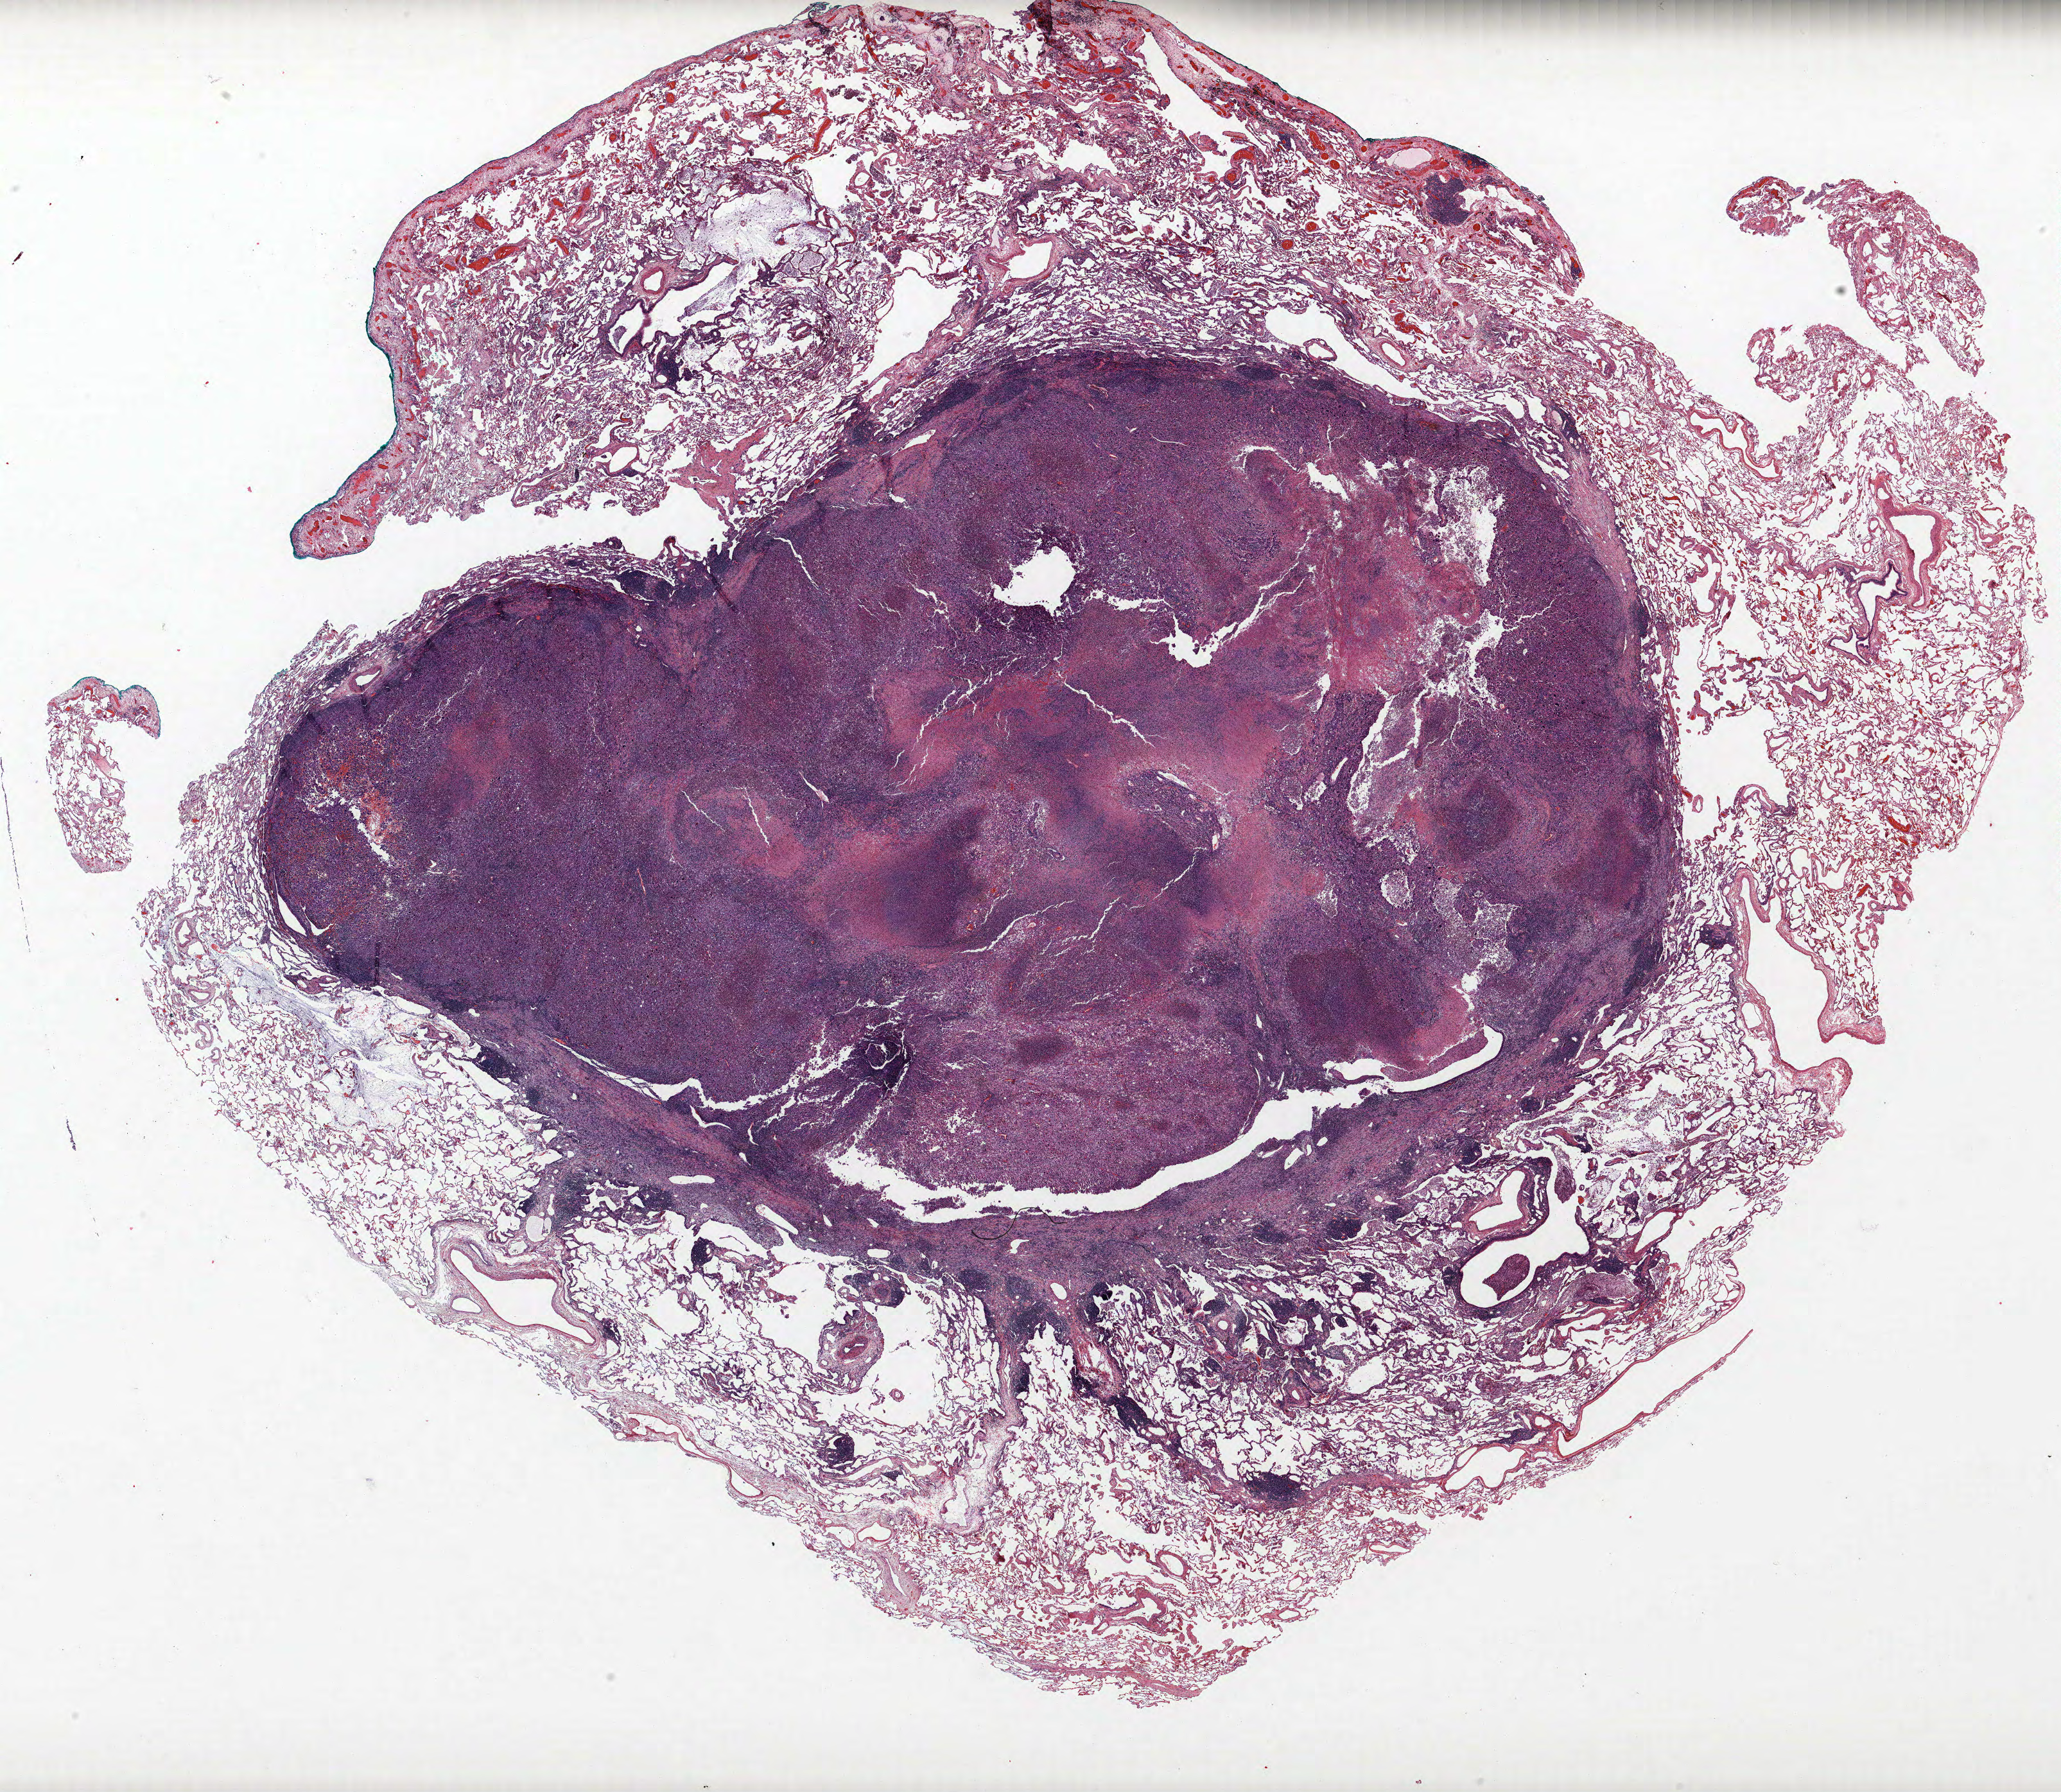
H&E-stained whole-slide image, whole scanned area (about 25.7 x 22.3 mm) shown as a low-resolution overview, FFPE section, lung tissue. Female, age 56 at enrolment. Current smoker at enrolment. Grade: poorly differentiated (G3).
- tumour size (pathology): 20 mm
- participant's lung-cancer diagnosis: Adenocarcinoma, NOS (ICD-O-3 8140/3)
- primary tumour location (clinical record): right upper lobe
- stage (AJCC 6th edition): IA